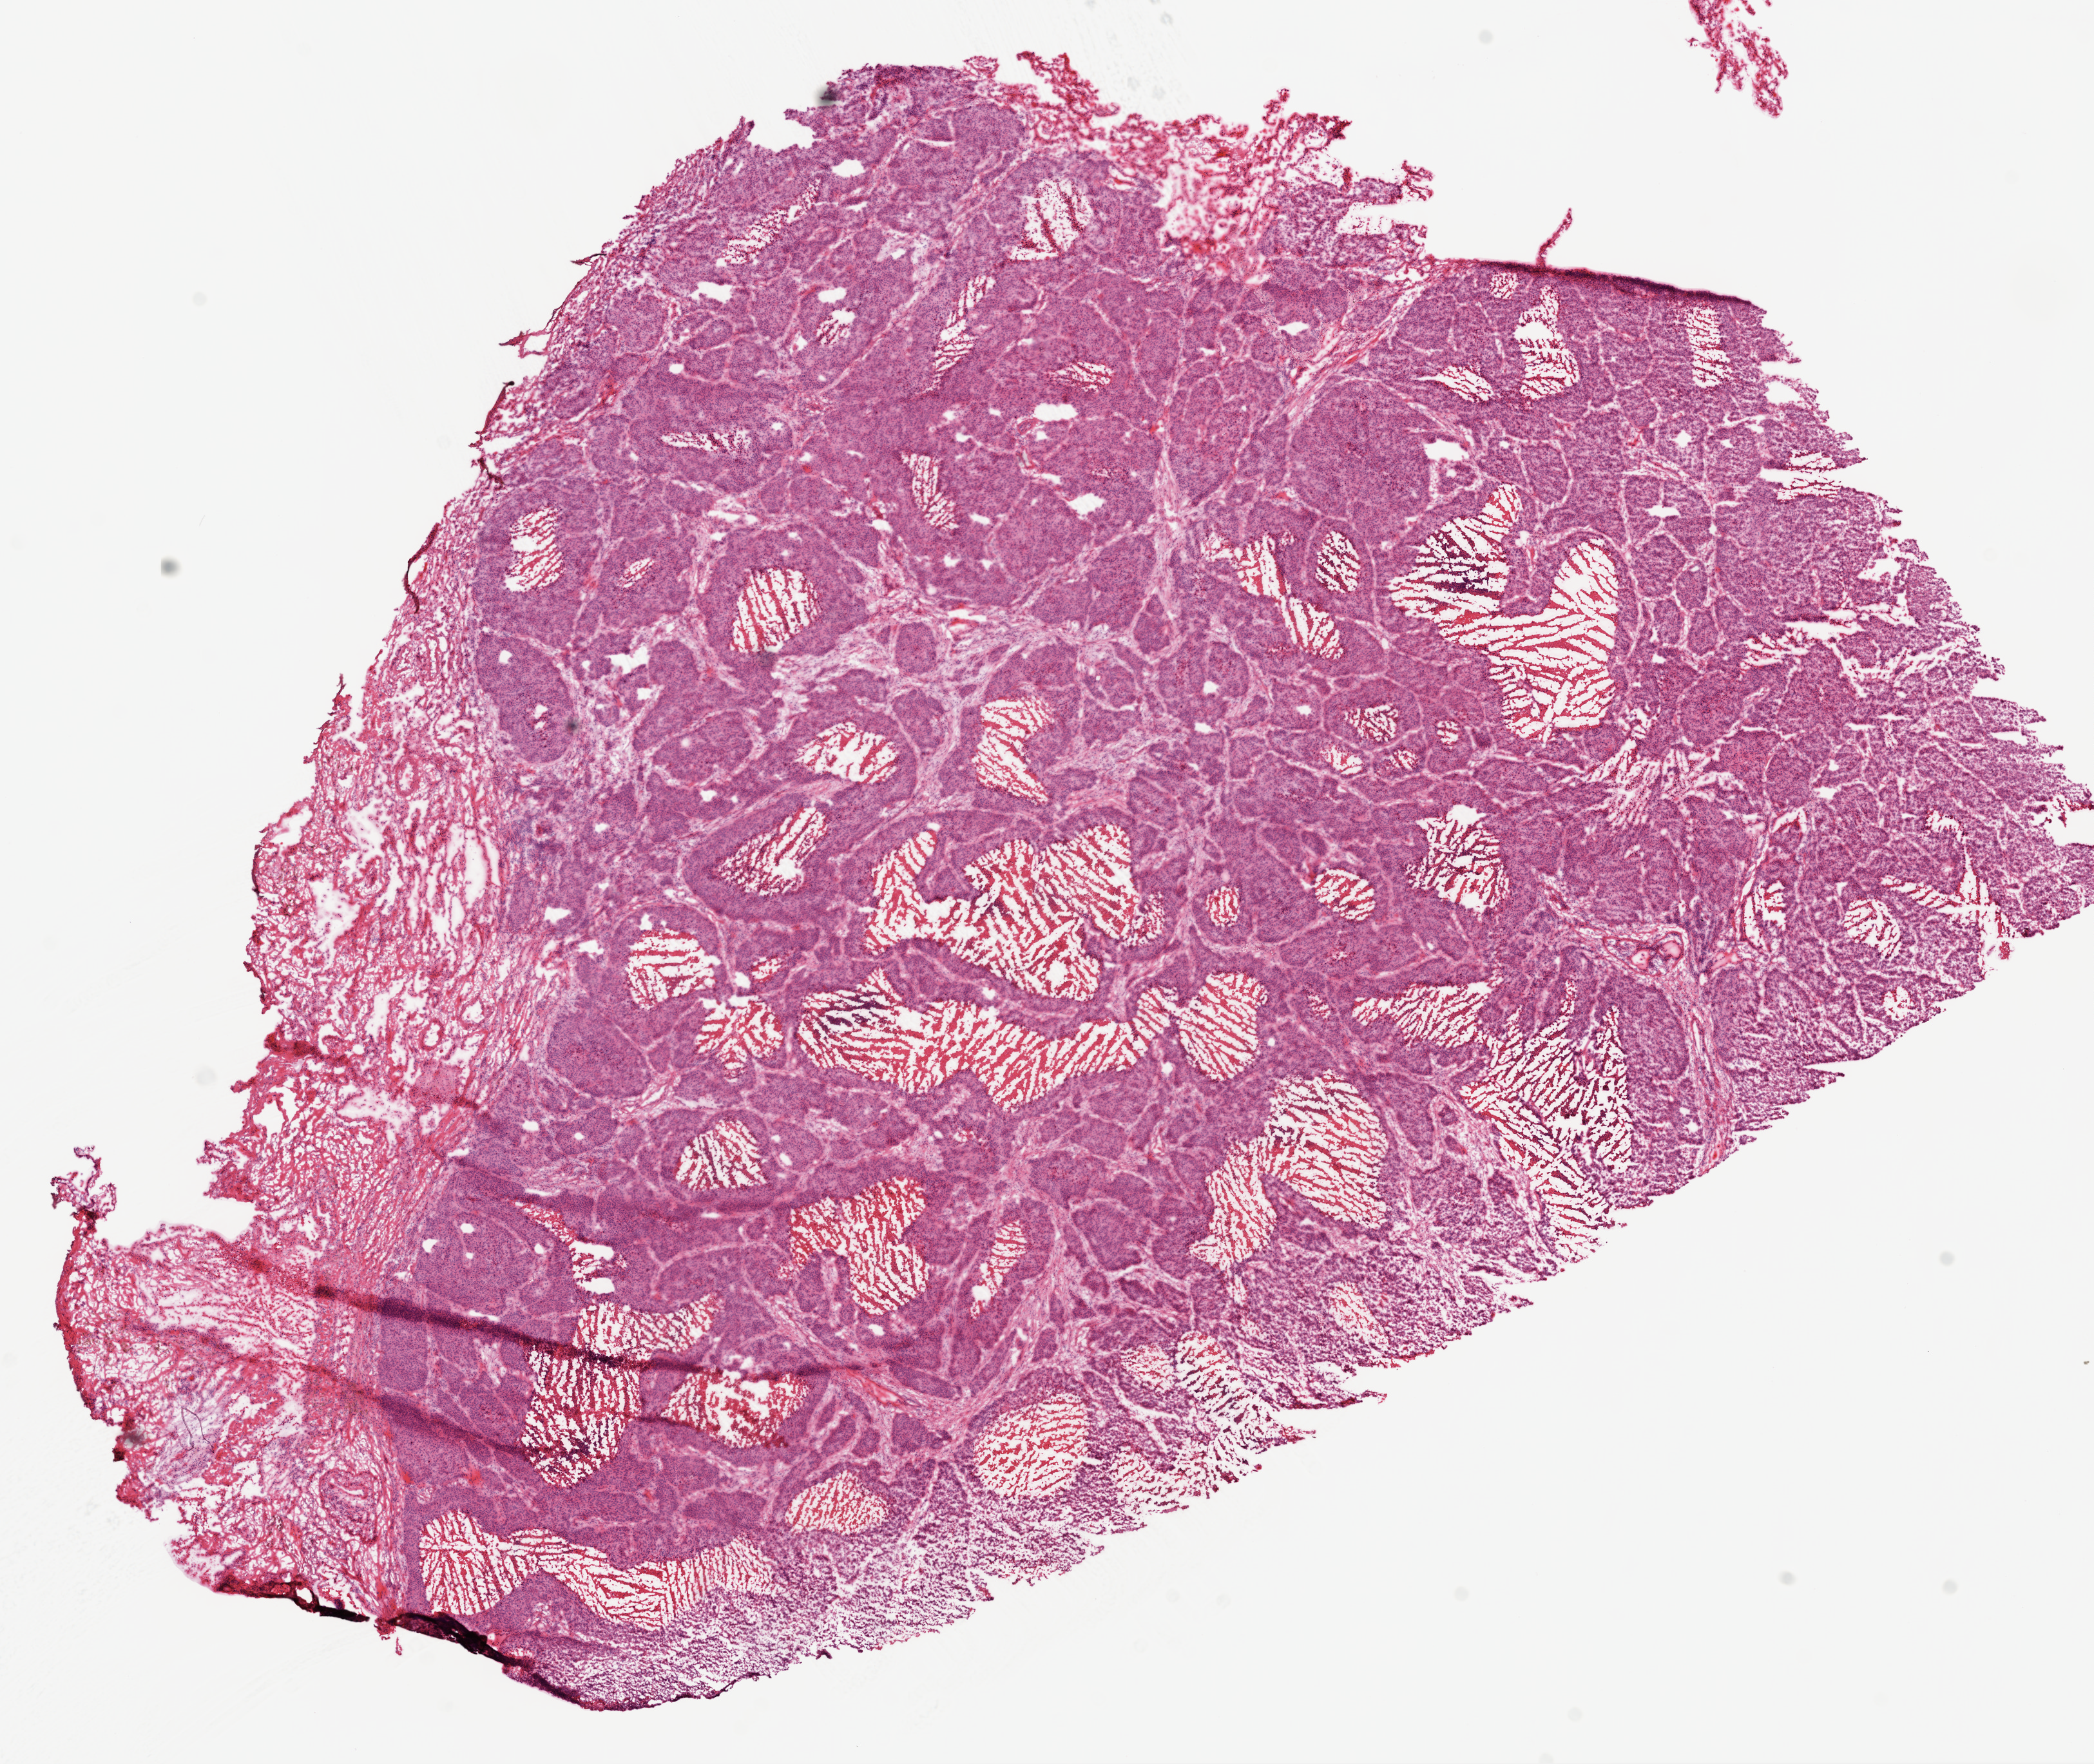
H&E whole-slide image, whole scanned area (about 13.0 x 11.0 mm, from a 20x scan) shown as a low-resolution overview, frozen section from the top of the tissue portion, sample: primary tumour, lung. Male, age 65 years at initial diagnosis. Slide review estimates, as recorded: tumour cells 70%, tumour nuclei 90%, normal cells 12%, stromal cells 5%, necrosis 13%.
- AJCC pathologic stage: IA
- diagnosis: Squamous cell carcinoma, NOS (lower lobe, lung)